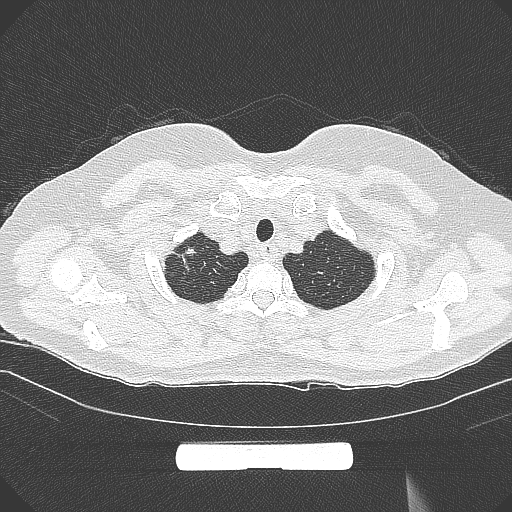
Chest CT, one axial slice; 120 kVp; lung window (W 1500 / L -600 HU); 1 mm slice thickness; 512 × 512 image matrix, field of view 369 × 369 mm. Female patient, age 58 years. From the clinical record (not read from this slice): clinical TNM (as recorded): T1b N0 M0; histopathological grade: G2-3.
Structures marked on this image (rectangle marked by the reading radiologist):
- lung tumour (recorded histology: adenocarcinoma): bounding box [x1, y1, x2, y2] px = [177, 244, 201, 275]